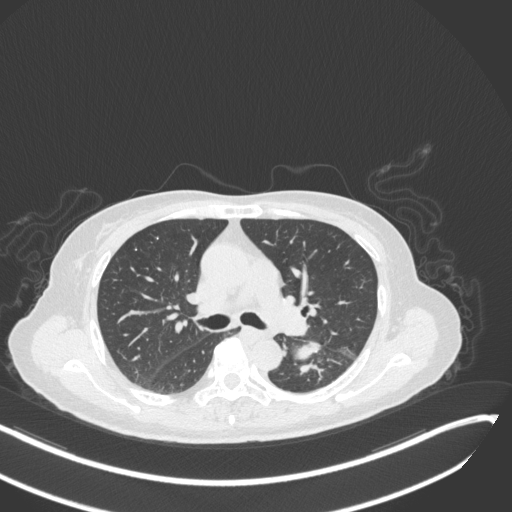
Chest CT, one axial slice. Position 177 of 342 along the scan axis. Reconstruction kernel B31f. 120 kVp. Lung window (W 1500 / L -600 HU). 512 × 512 image matrix, field of view 400 × 400 mm. Female patient, age 64 years. From the clinical record (not read from this slice): clinical TNM (as recorded): T3 N1 M1.
Structures marked on this image (bounding box drawn by a radiologist):
- lung tumour (recorded histology: small cell carcinoma): bounding box (x1, y1, x2, y2) in pixels: (287, 335, 325, 365)